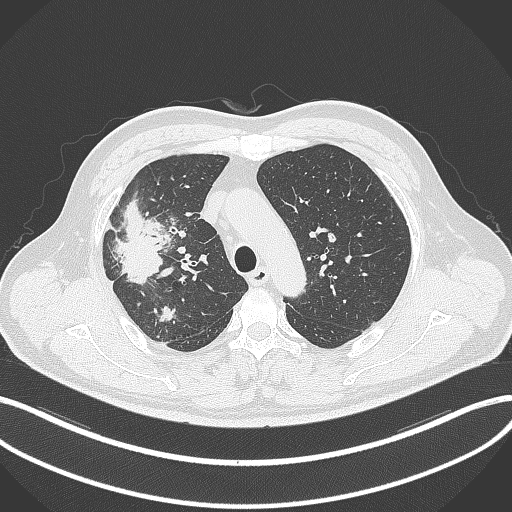
Chest CT, one axial slice; slice 249 of 348 in the series (ordered by position); lung window (W 1500 / L -600 HU); 1 mm slice thickness; 512 × 512 image matrix. Patient: male, 55 years. Case-level facts recorded for this patient, not image findings: clinical TNM (as recorded): T3 N2 M1.
Annotated regions visible in this slice (rectangle marked by the reading radiologist):
- lung tumour (recorded histology: adenocarcinoma): box from (x=113, y=199) to (x=169, y=285) px